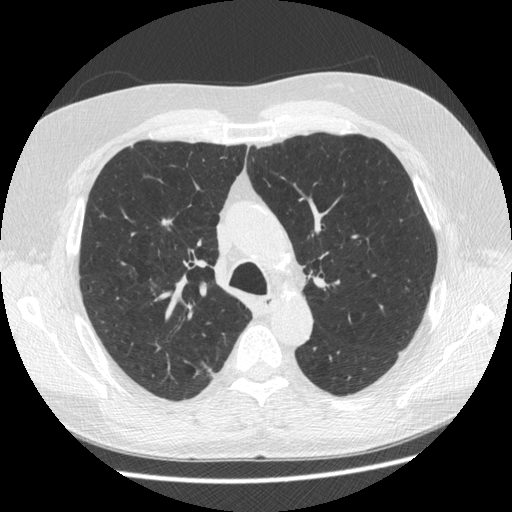
Axial slice from a low-dose chest CT screening exam; third annual screen; lung window (W 1500 / L -600 HU); 1.25 mm slice thickness. Male, age 63 years at enrolment. Former smoker at enrolment.
- Expert-annotated lung lesion, bounding box [x1, y1, x2, y2] px = [150, 208, 183, 237].
- The screening reader recorded 2 non-calcified nodules or masses ≥4 mm on this exam (right upper lobe, left upper lobe); which of them this box marks is not recorded.
- Official screen result: positive, other.
- Participant outcome: lung cancer diagnosed 342 days after this screen — adenocarcinoma, NOS, right upper lobe, stage IIA (AJCC 6th edition), 8 mm at pathology.